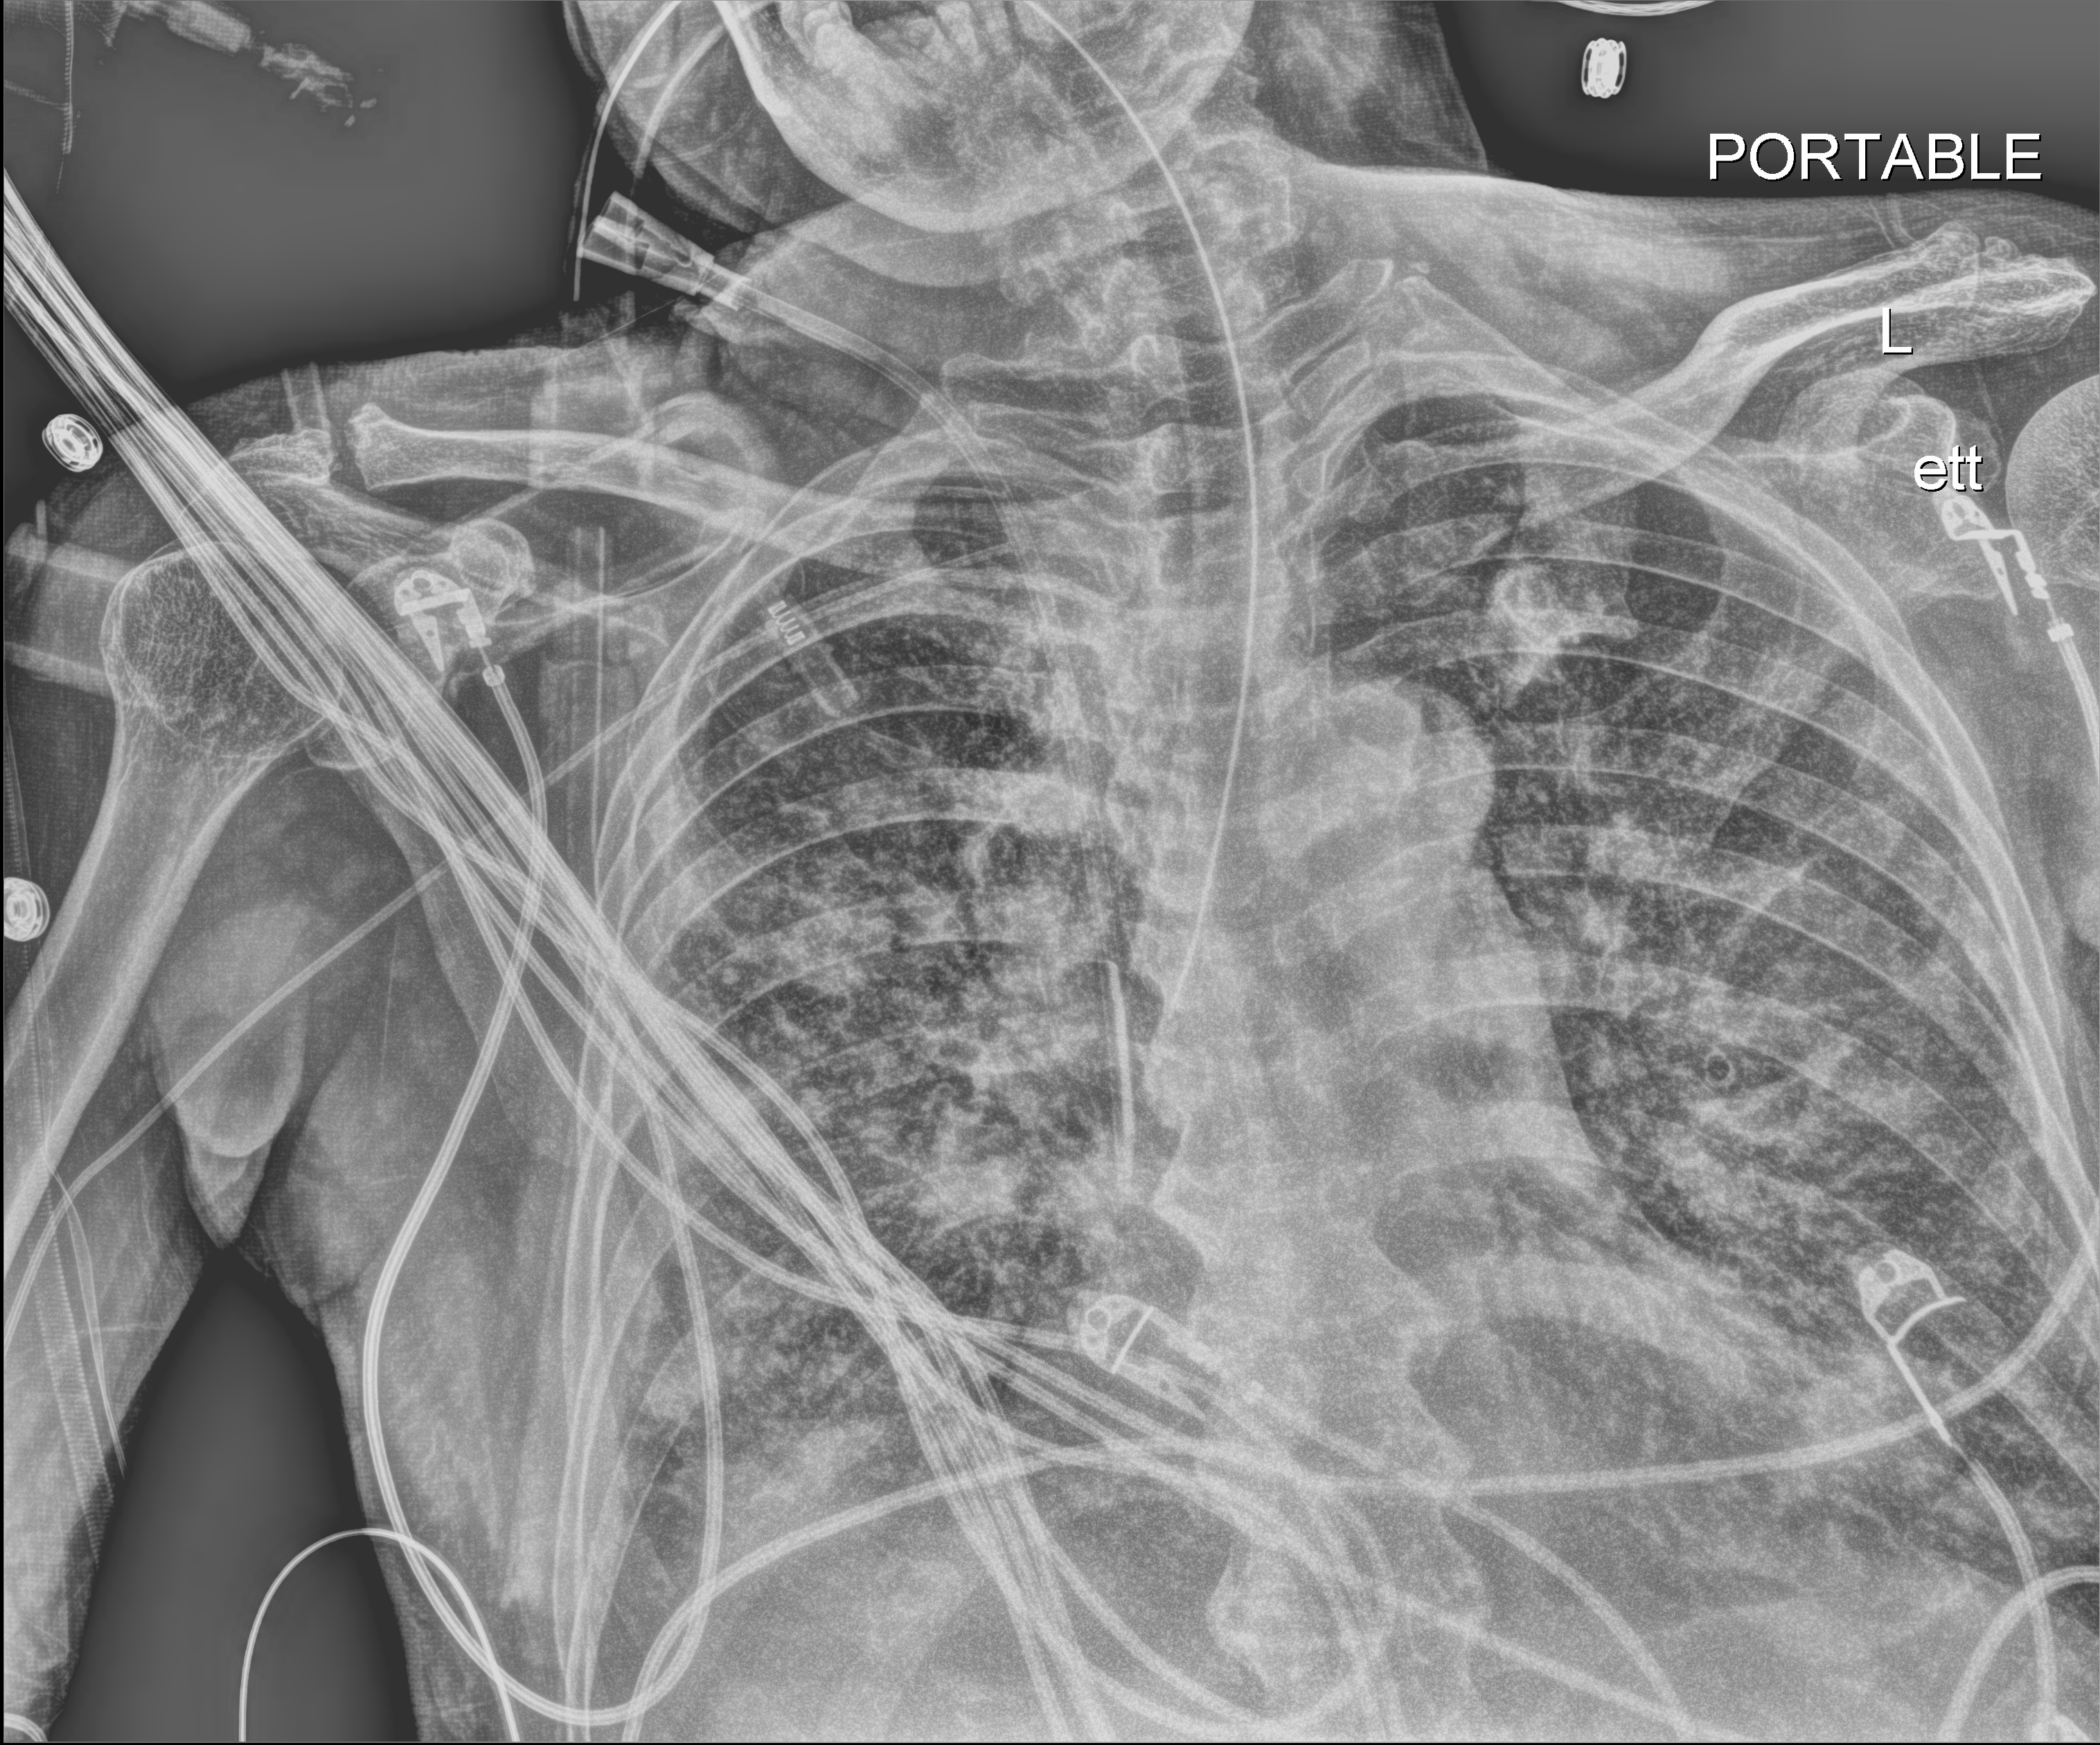
Chest radiograph (digital radiography); anteroposterior (AP) projection. Male patient hospitalised with COVID-19, age 60–74 years.
From the hospital-stay record, not from the radiograph (when in the stay this image was taken is not recorded): mechanically ventilated during this hospital stay: yes.